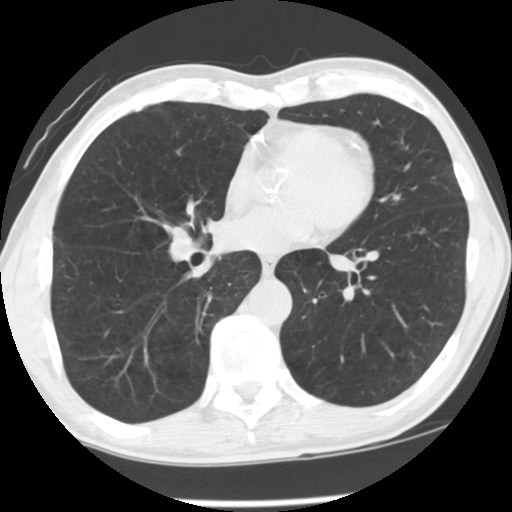
Low-dose screening chest CT, axial slice; third screening round (two years after baseline); lung window (W 1500 / L -600 HU); 2.5 mm slice thickness; standard (soft-tissue) reconstruction kernel (STANDARD); slice 79 of 139 in the series; 512 × 512 image matrix. Male participant, aged 63 years at enrolment.
Lesion marked by an expert reader, bounding box [x1, y1, x2, y2] px = [404, 217, 438, 248]. Screening reader's record for this exam (one nodule recorded; not confirmed to be the boxed lesion): non-calcified nodule or mass ≥4 mm, left lower lobe, 6 × 5 mm, smooth margins, soft tissue attenuation, pre-existing on the prior screen: no. Official screen result: positive, other. Lung cancer was diagnosed 269 days after this screen: squamous cell carcinoma, NOS, left lower lobe, poorly differentiated (G3), stage IA (AJCC 6th edition), 4 mm at pathology.